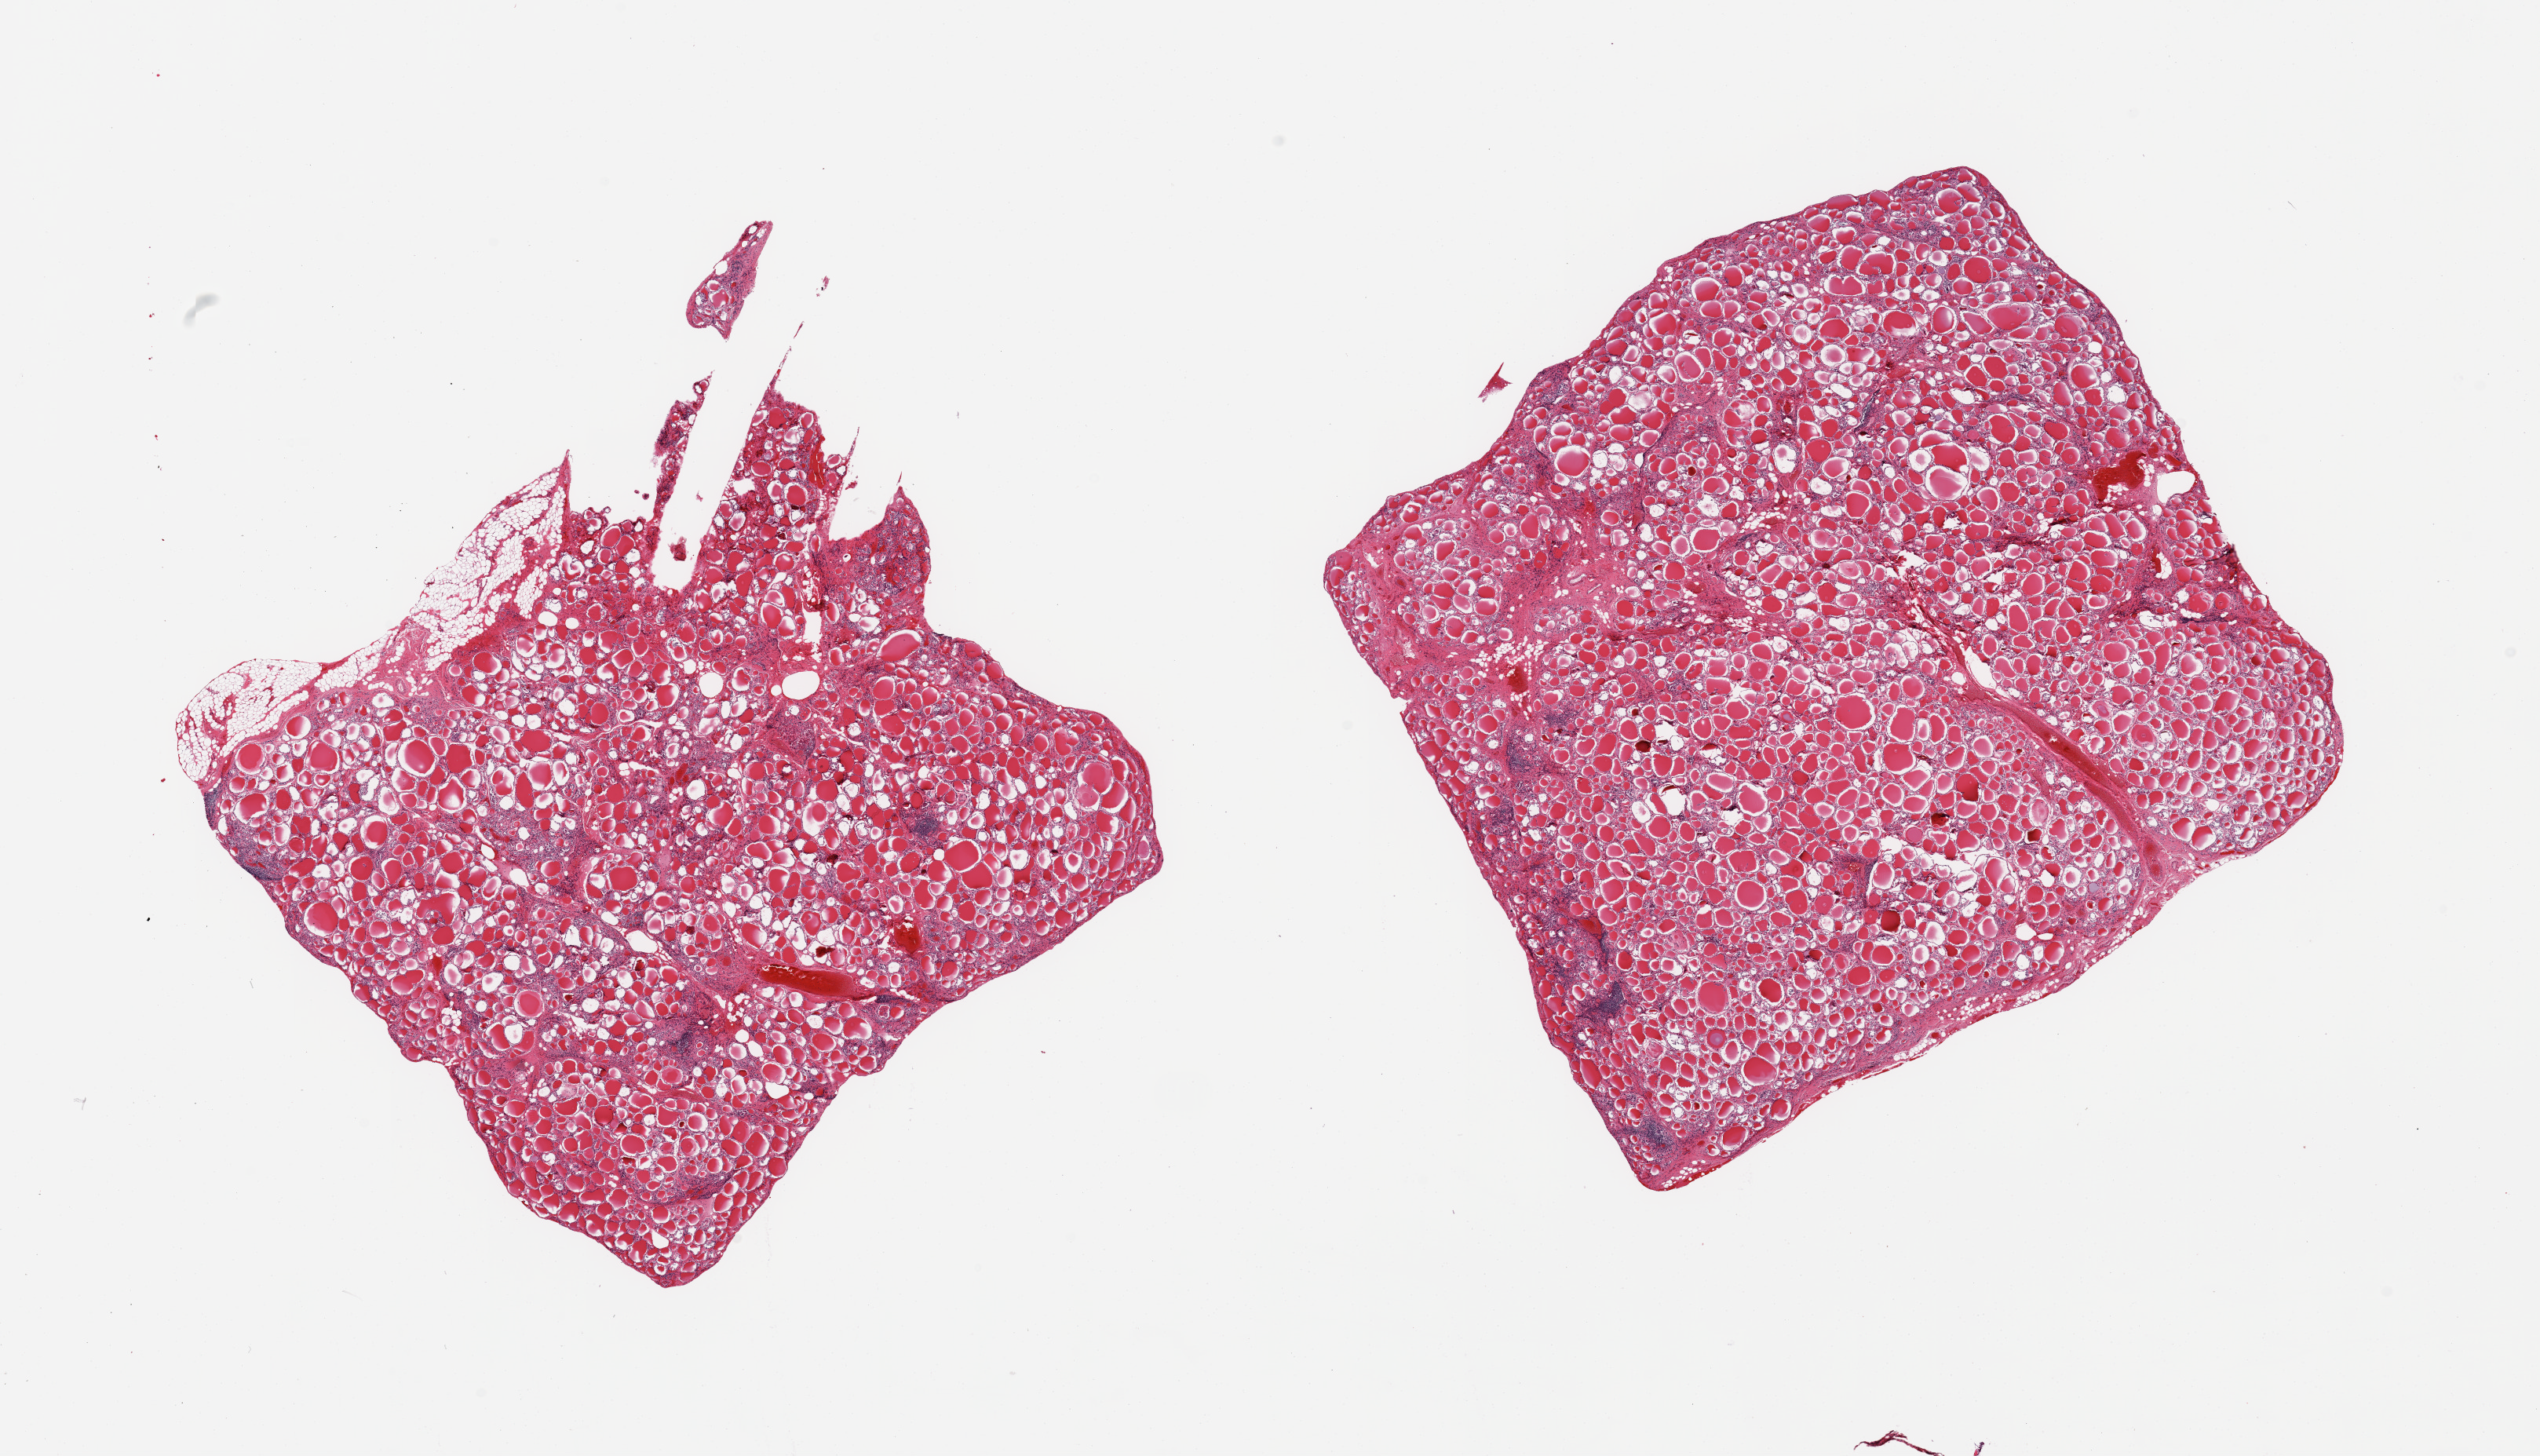
Digitized H&E-stained section, low-resolution overview of the scanned area, about 25.6 x 14.7 mm. PAXgene-fixed, paraffin-embedded tissue. Section of thyroid (target tissue). Donor tissue sample. Donor: male.
Reviewer comment on this tissue sample: 2 pieces; slight focal lymphoid deposits c/w lymphocytic thyroiditis.